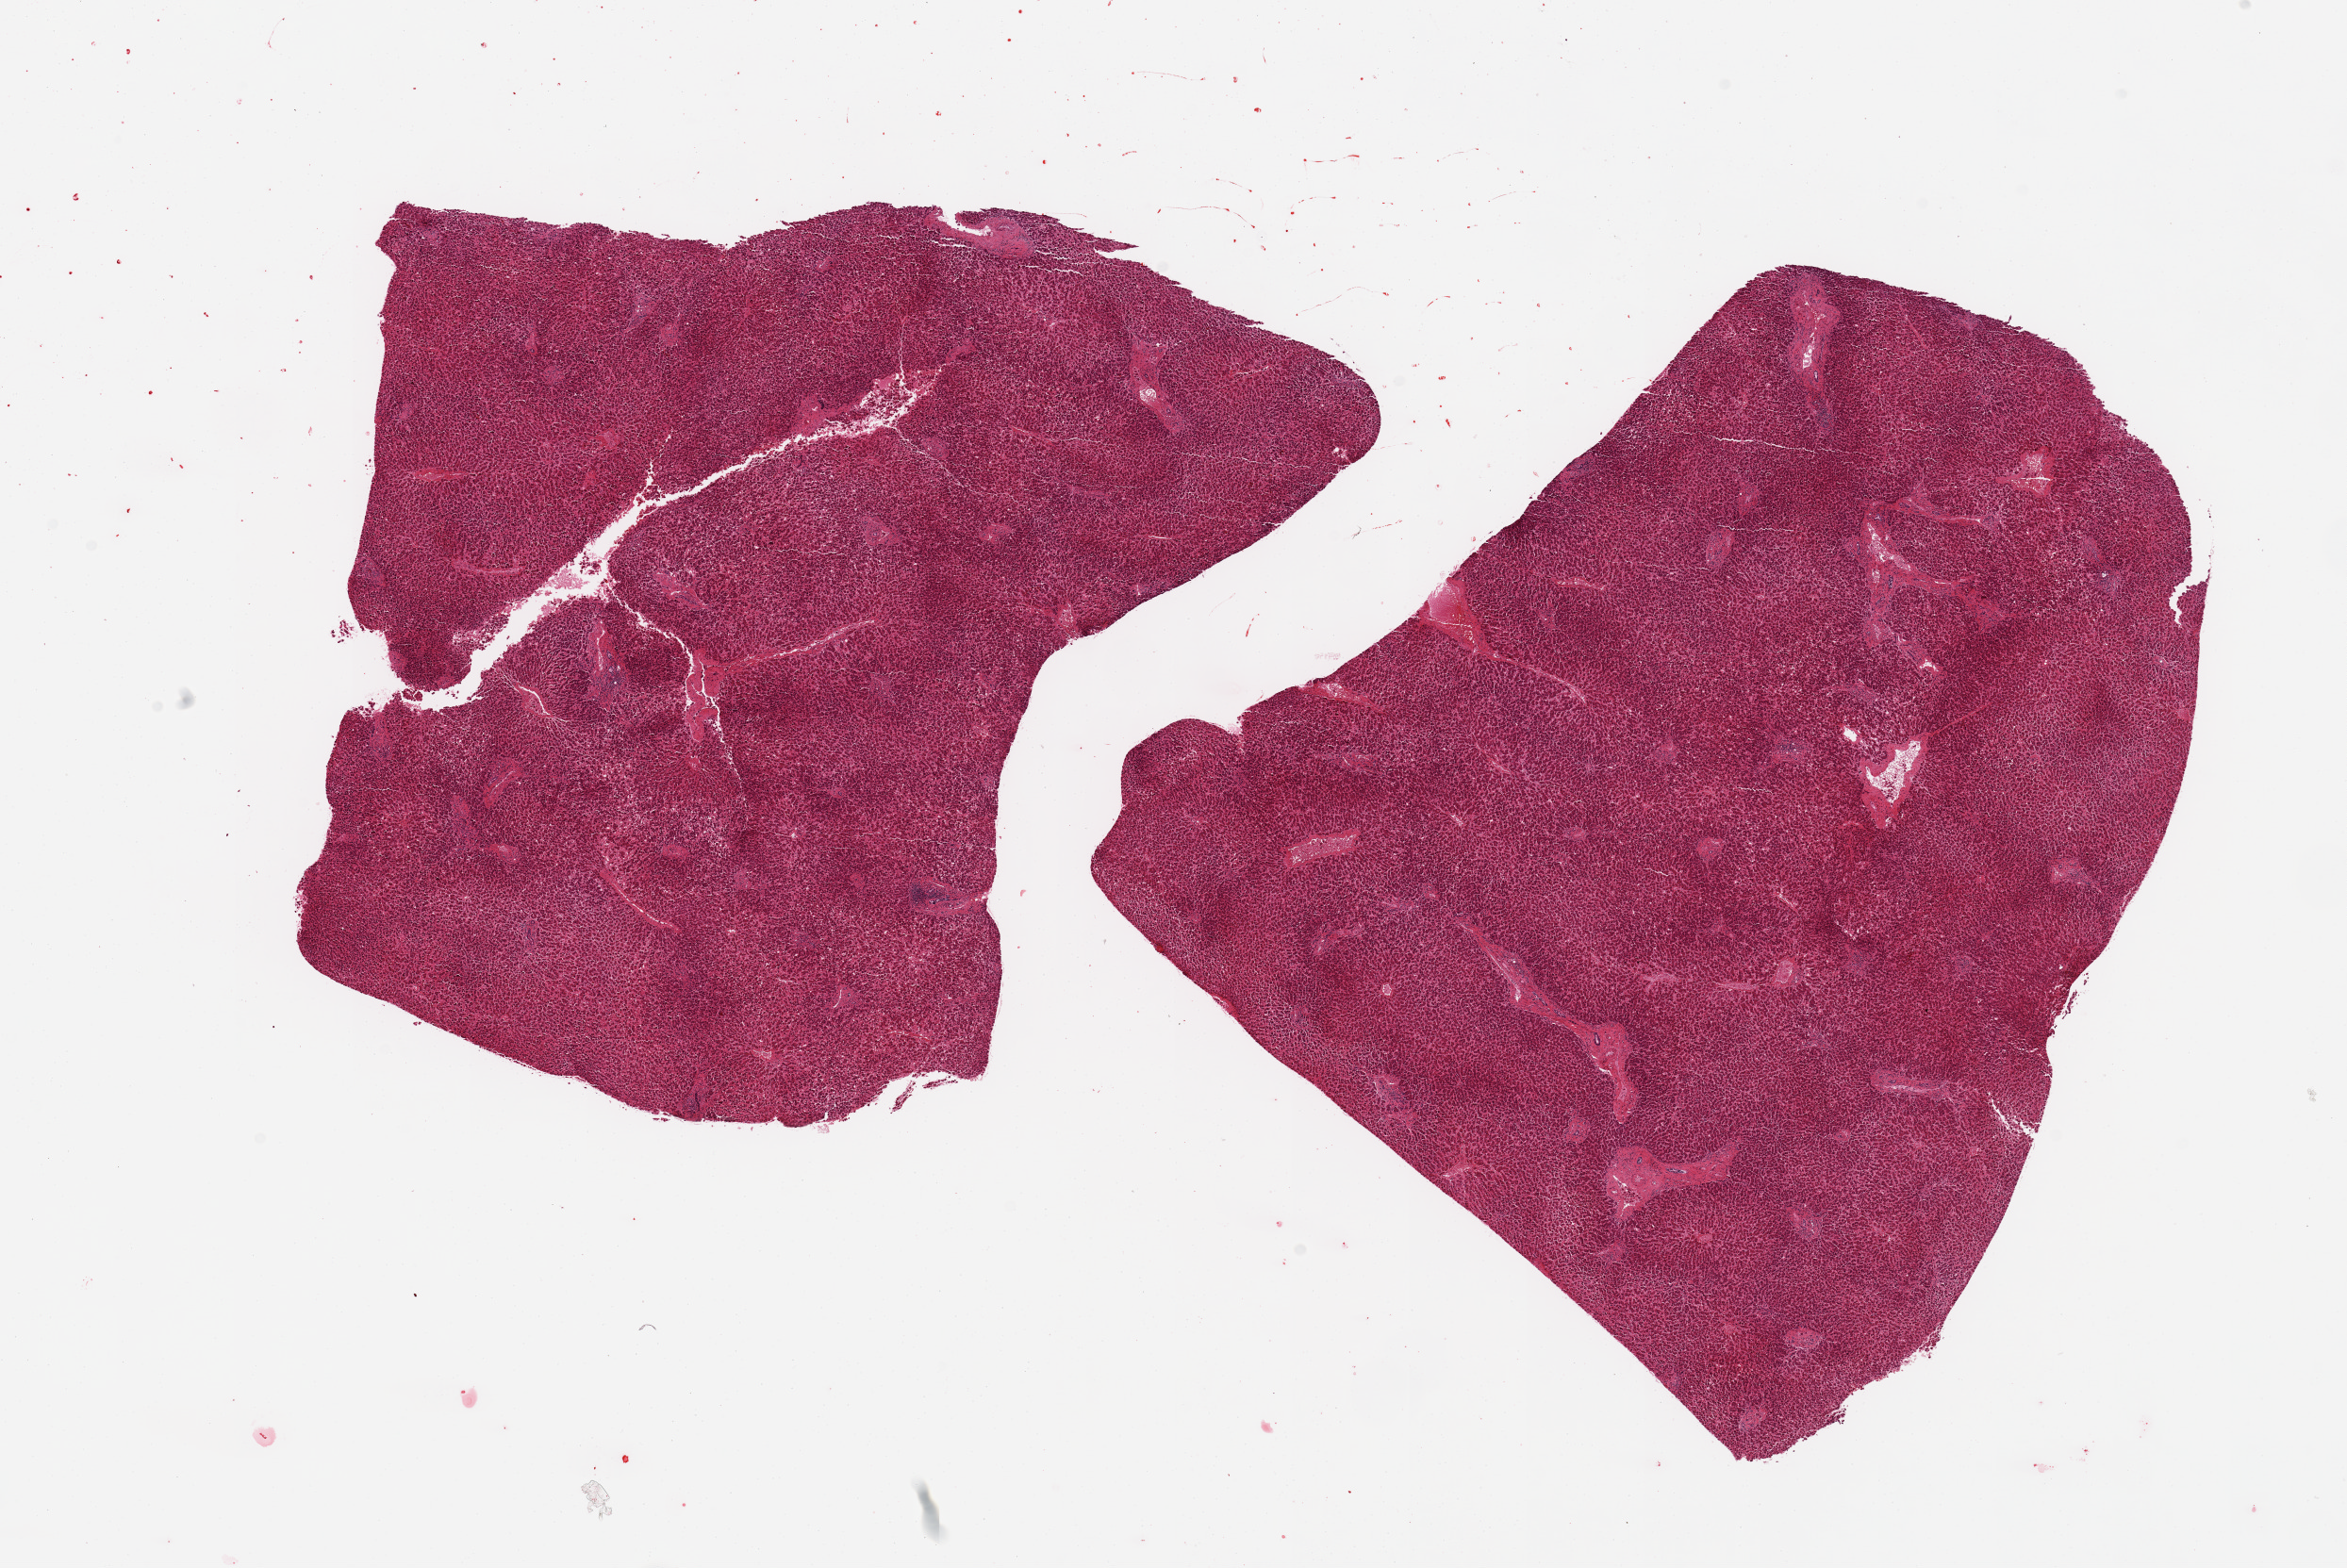
Whole-slide image, hematoxylin and eosin (H&E) stain, brightfield, shown as a low-resolution overview of the whole scanned area (about 19.7 x 13.2 mm, acquisition: 20x scan), PAXgene-fixed paraffin-embedded (PFPE) section, target tissue: liver, tissue donor sample. Donor: female.
* pathologist's review note for this sample: 2 pieces, mild - moderate congestion